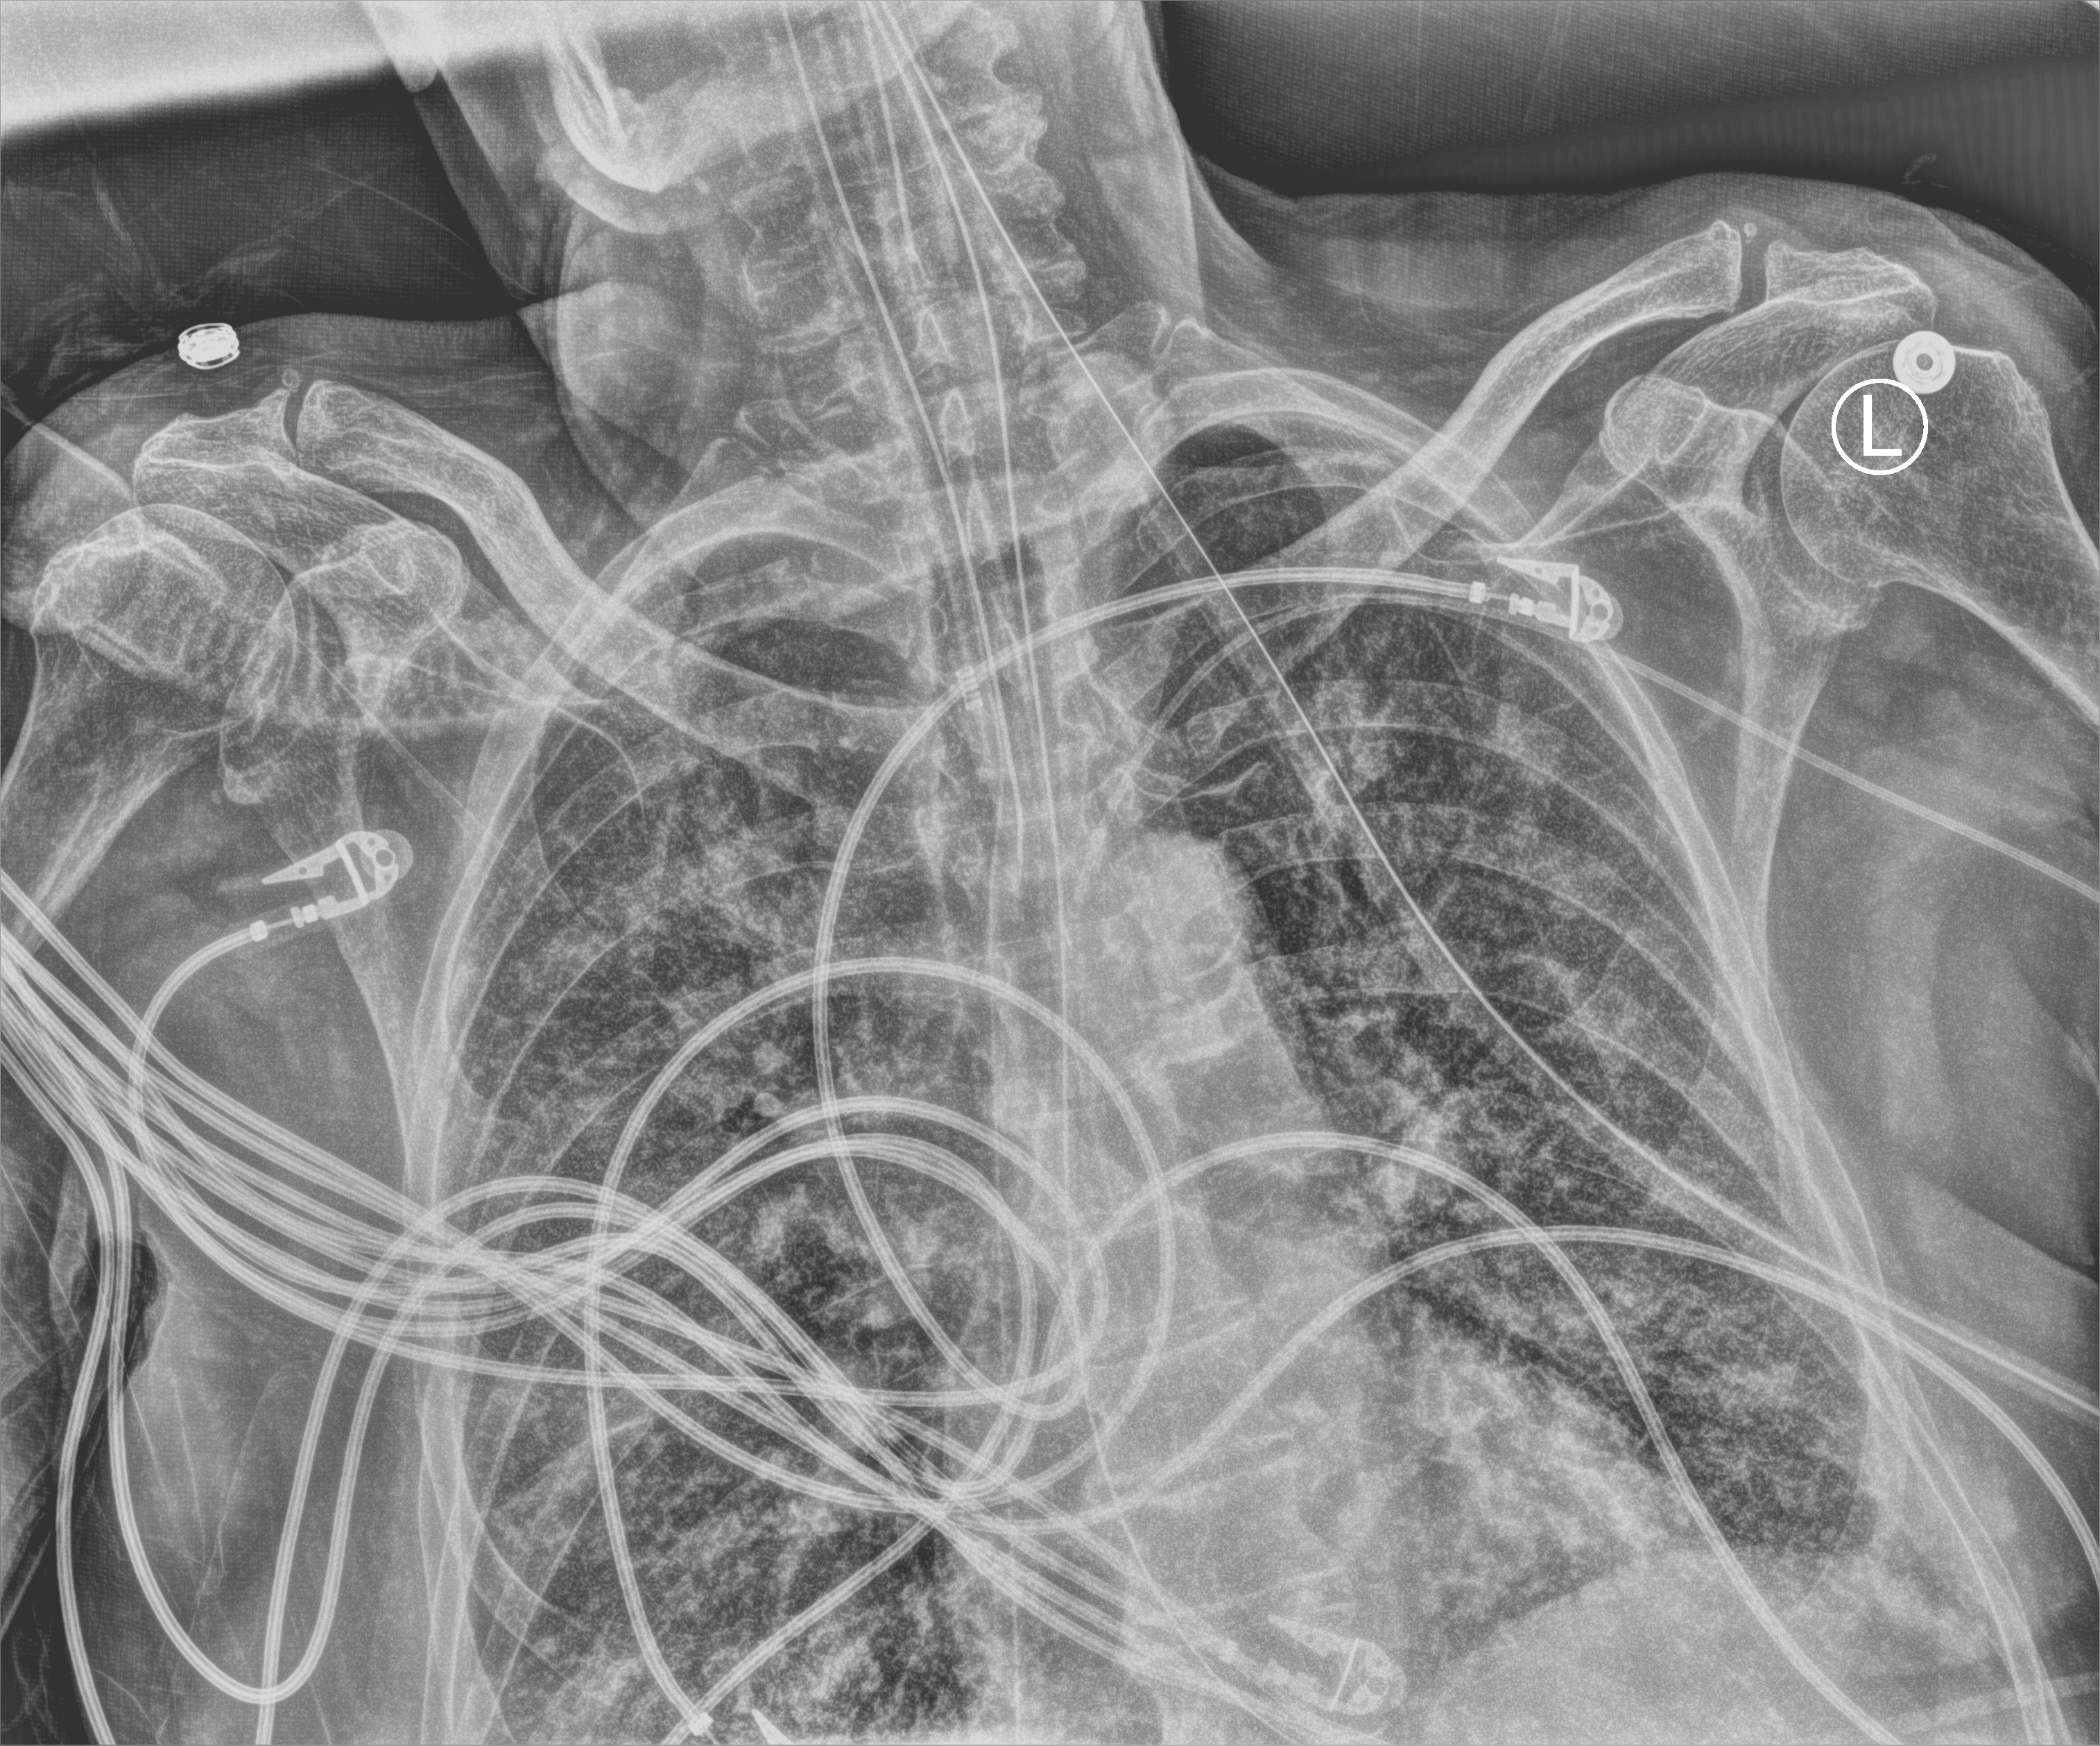
Bedside chest radiograph (computed radiography), anteroposterior (AP) projection. Patient hospitalised with COVID-19; male, aged 75–90 years.
Hospital-stay facts (about this admission, not read from this image; timing relative to this image not recorded):
- mechanically ventilated during this hospital stay: yes
- diabetes (admission record): no